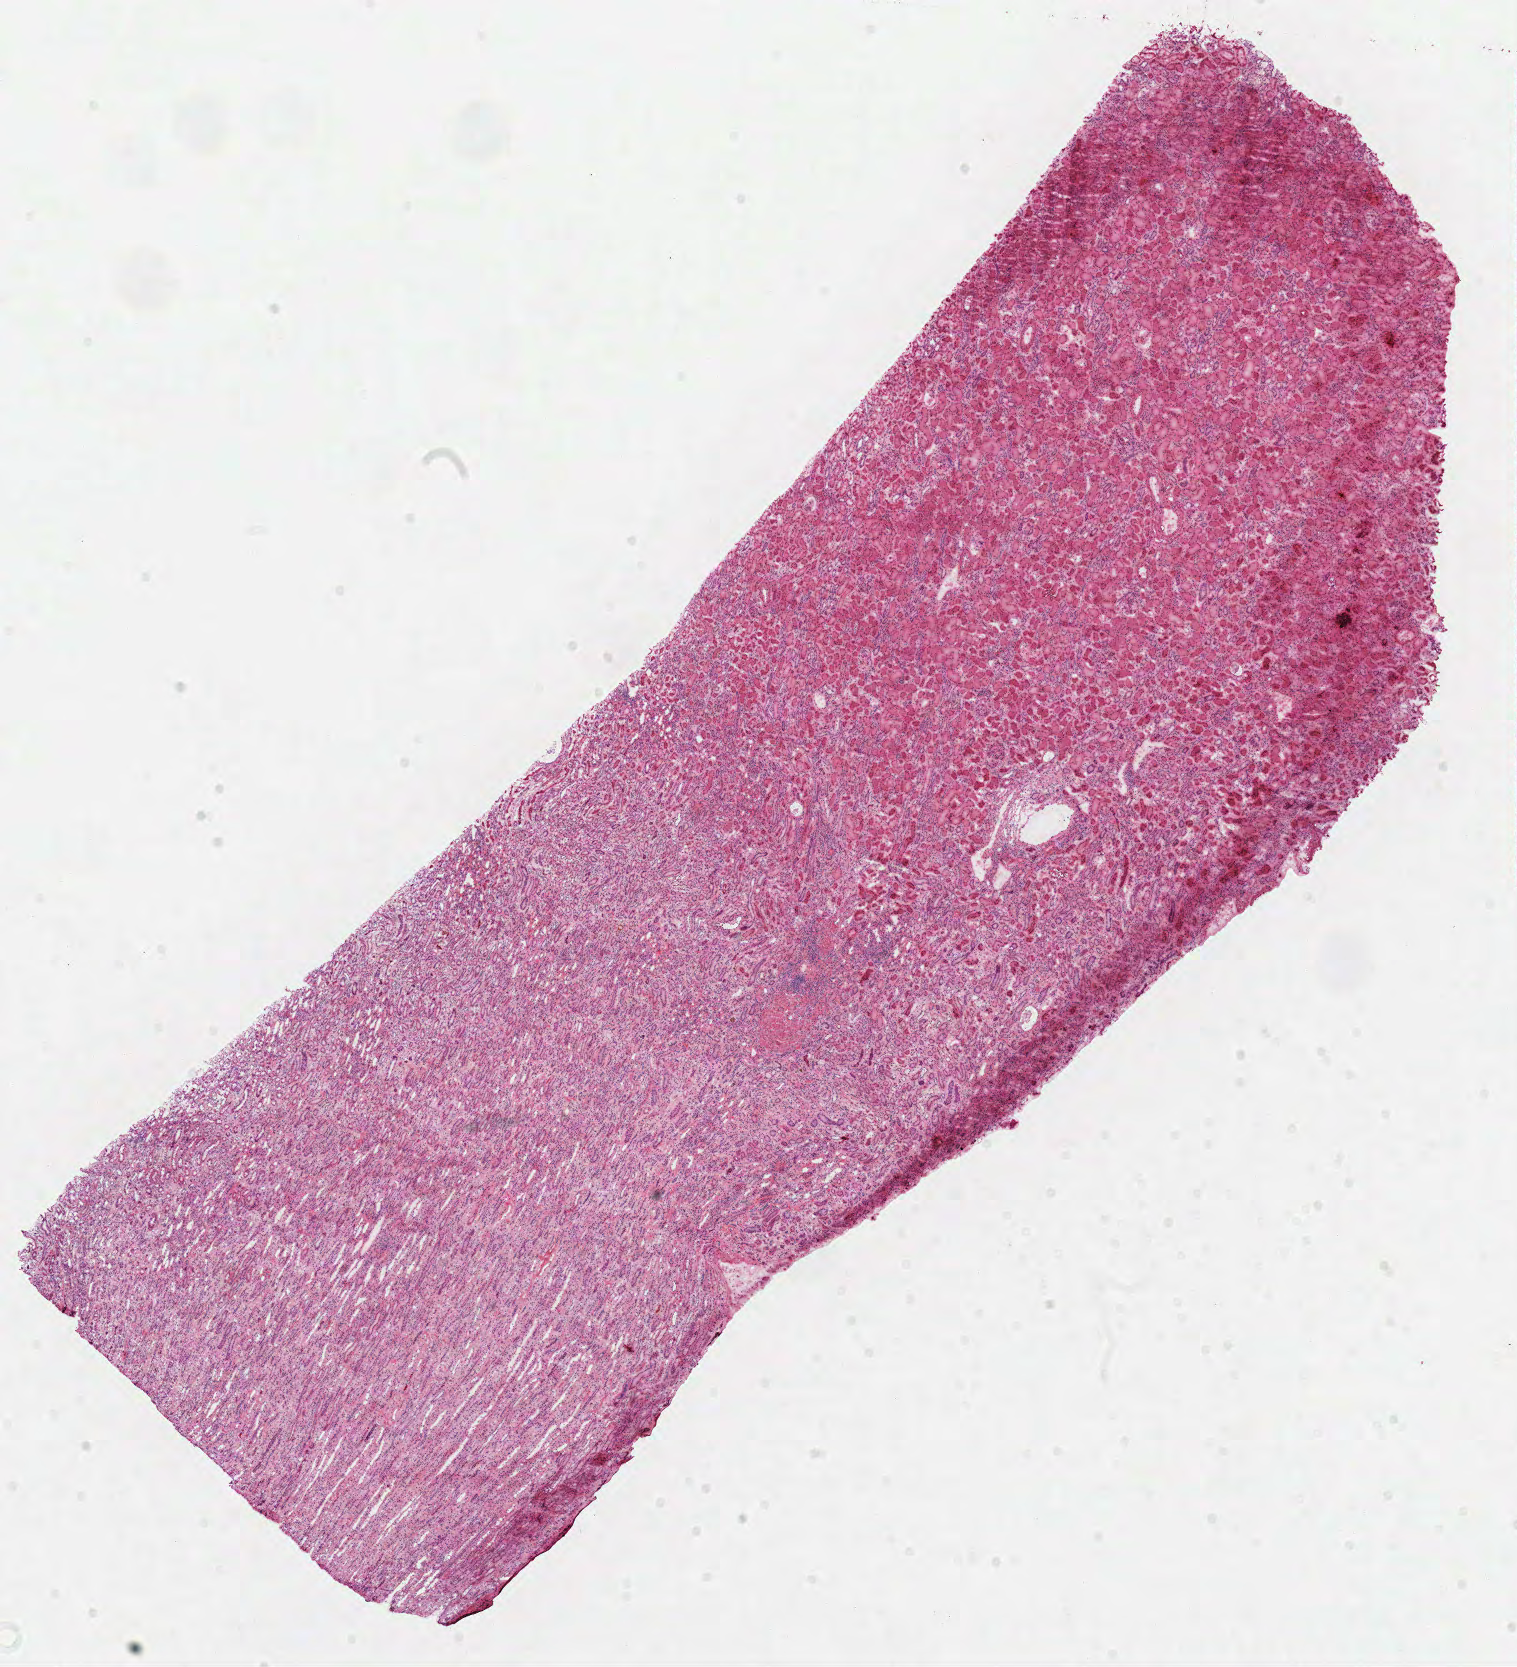
Hematoxylin and eosin (H&E) stained whole-slide image — shown as a low-resolution overview of the whole scanned area (about 12.0 x 13.1 mm, acquisition: 40x scan). Frozen section from the top of the tissue portion. Solid tissue normal (non-tumour tissue) sample from the kidney. Male, age 73 years at initial diagnosis.
This section: solid tissue normal (non-tumour) sample from the same patient. Patient diagnosis: Clear cell adenocarcinoma, NOS.